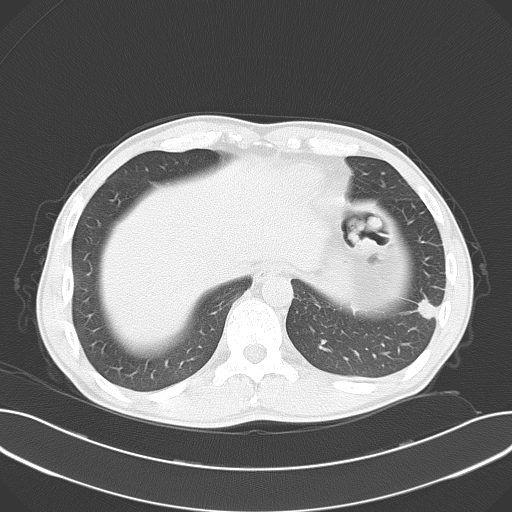
Chest CT, one axial slice. Position 15 of 62 along the scan axis. Lung window (W 1500 / L -600 HU). 5 mm slice thickness. 512 × 512 image matrix. Male patient, age 44 years. From the clinical record (not read from this slice): clinical TNM (as recorded): T1c N0 M1b.
Annotated regions visible in this slice (bounding box drawn by a radiologist):
- lung tumour (recorded histology: adenocarcinoma): box from (x=412, y=295) to (x=443, y=325) px